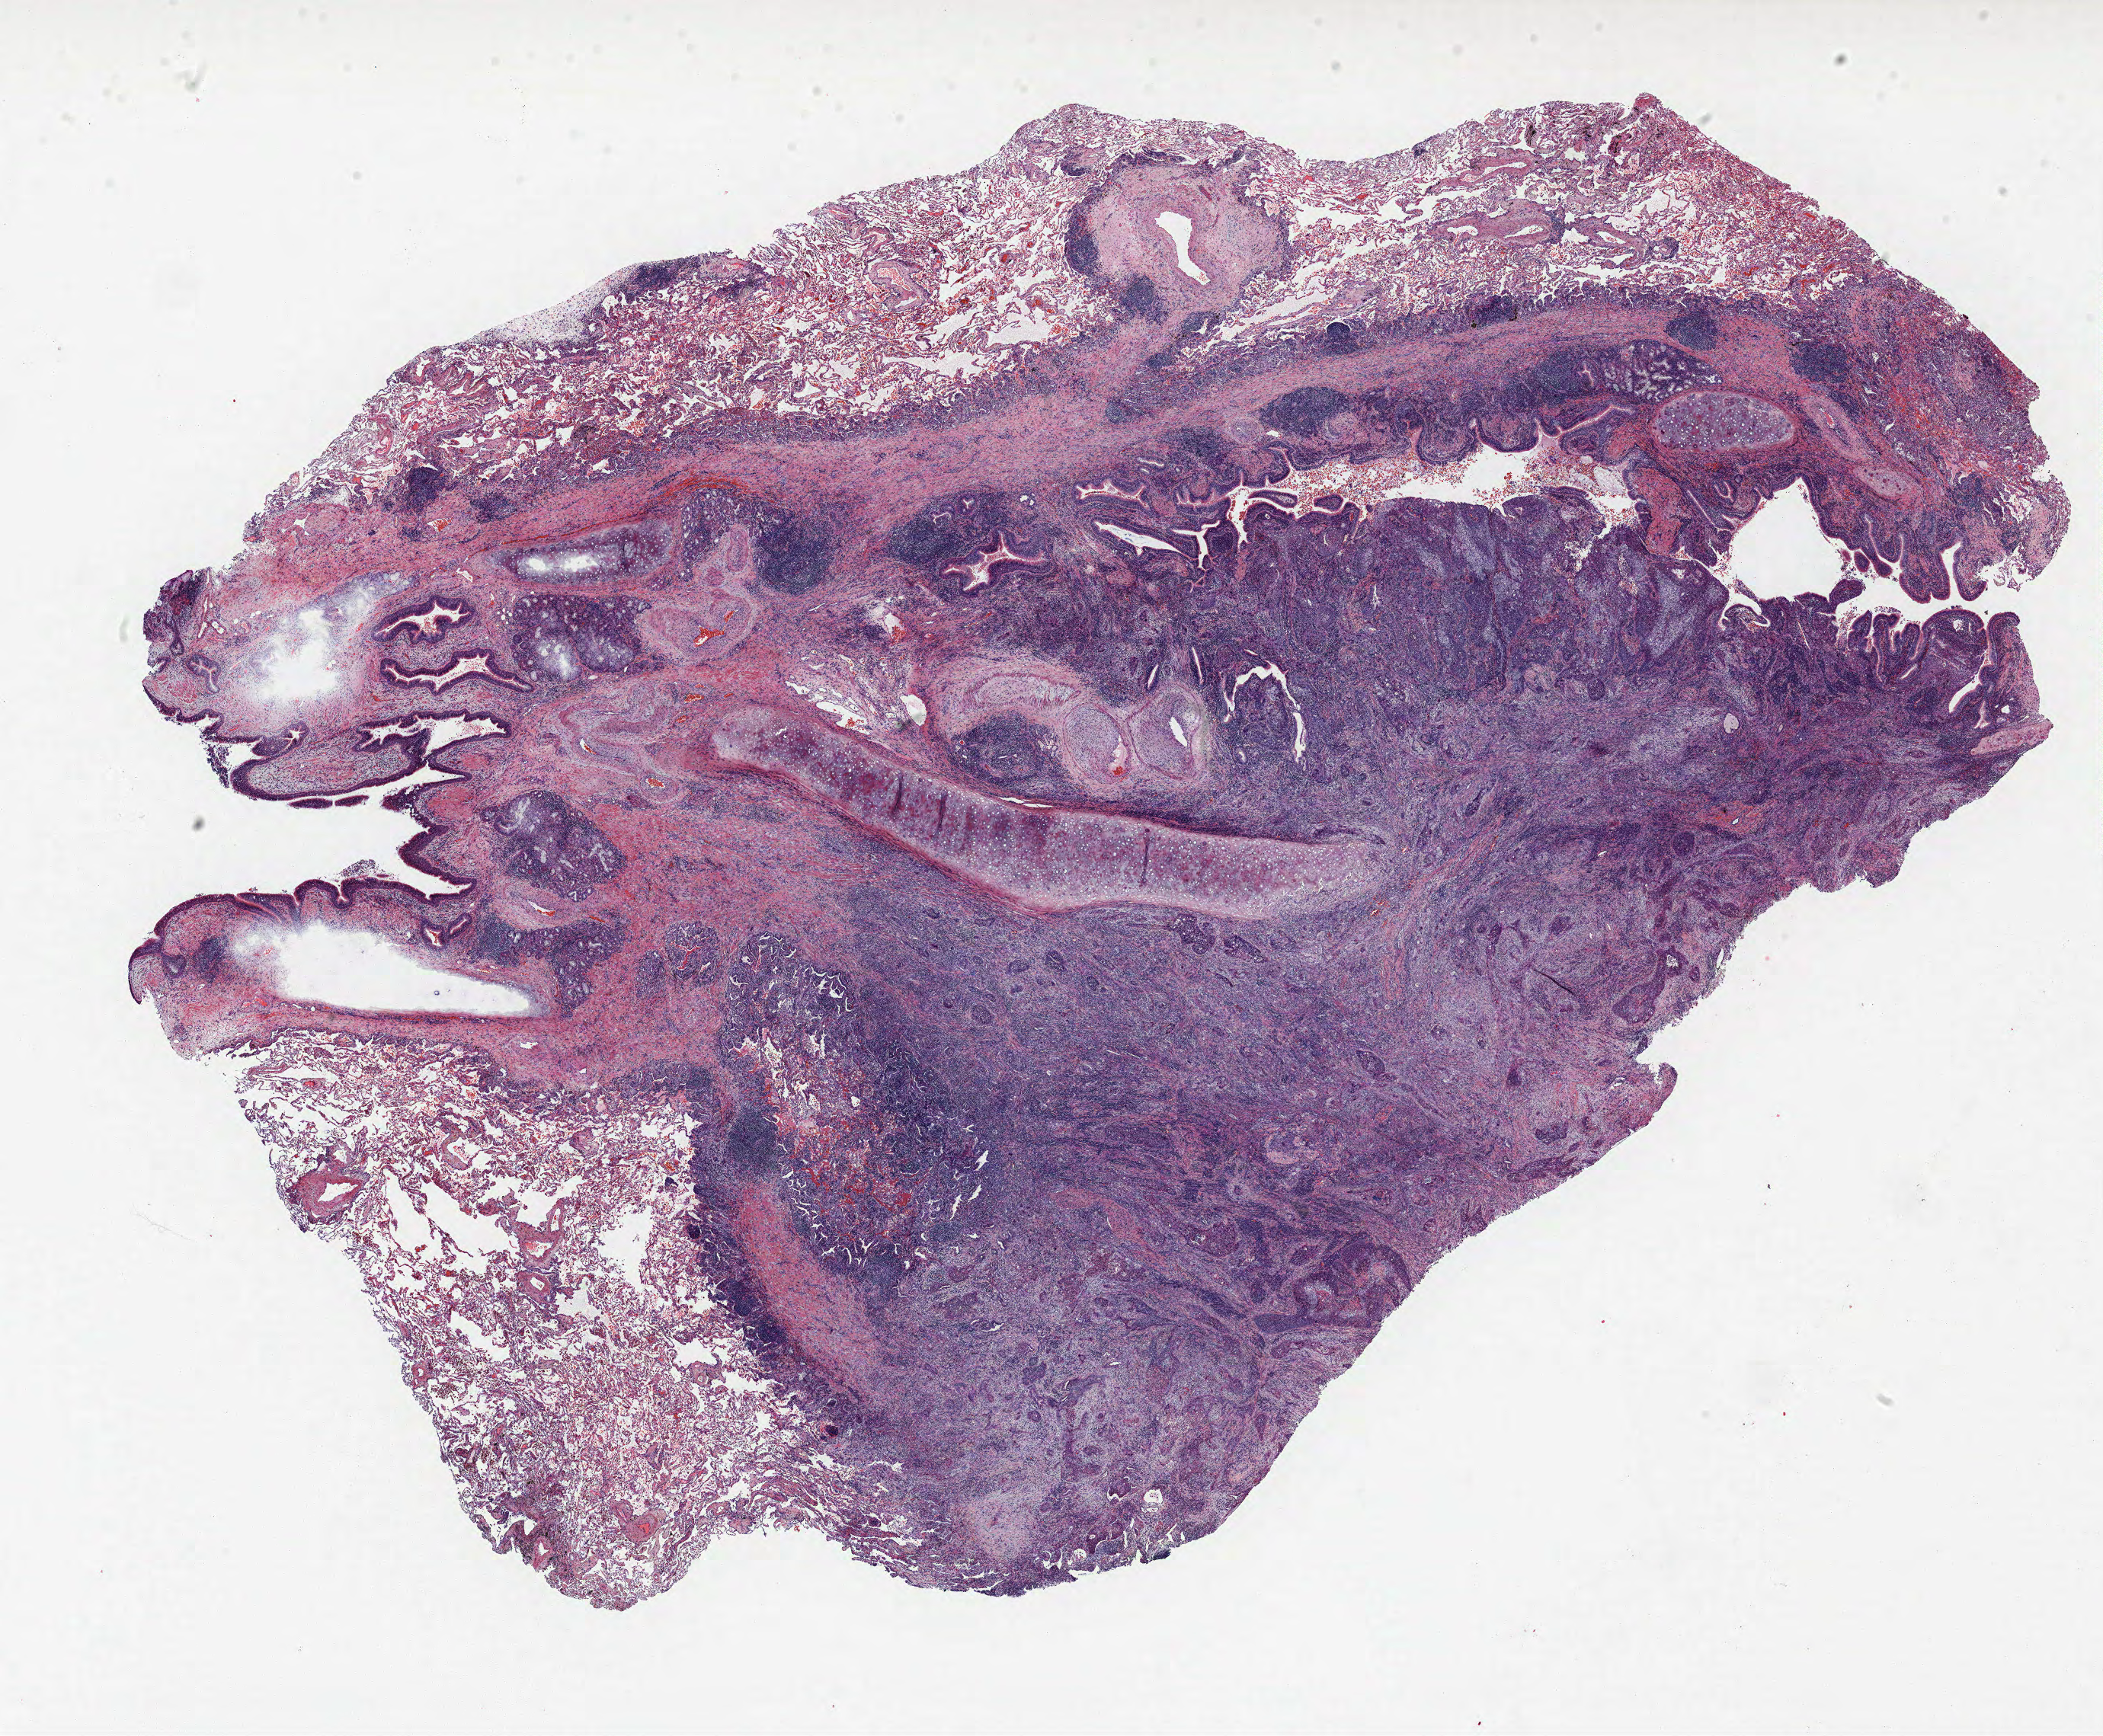
Whole-slide histology image, H&E, low-resolution overview of the scanned area, about 22.1 x 18.2 mm (from a 40x scan). FFPE section. Lung. Male patient, aged 68 at enrolment. Current smoker at enrolment. Grade: poorly differentiated (G3).
ICD-O-3 topography: upper lobe of lung (C34.1). Tumour size (pathology): 20 mm. Stage (AJCC 6th edition): IA. Participant's lung-cancer diagnosis: Squamous cell carcinoma, NOS. Primary tumour location (clinical record): left upper lobe.